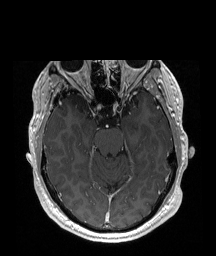
Brain MRI from a brain-tumour surgery series, one axial slice. Position 125 of 192 along the scan axis. T1-weighted post-contrast. 1 mm slice thickness. 216 × 256 image matrix, field of view 219 × 260 mm. From the clinical record (not read from this slice): histopathology: Astrocytoma; WHO grade: 2; IDH mutation: yes; tumour location: Right Insular.
Annotated regions visible in this slice (expert manual segmentation):
- tumour: bounding box (x1, y1, x2, y2) in pixels: (69, 93, 91, 114)